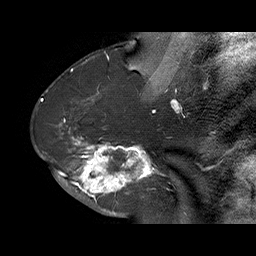
Breast MRI (dynamic contrast-enhanced), one sagittal slice; slice 35 of 70 in the series (ordered by position); dynamic contrast-enhanced series, time point 2 of 6 at this slice position (early post-contrast); 1.5 T; TE 4.5 ms, TR 32.4 ms; 3 mm slice thickness; 256 × 256 image matrix, field of view 180 × 180 mm. Female patient. From the clinical record (not read from this slice): setting: breast cancer imaged before/during neoadjuvant chemotherapy; receptor status: HR-positive, HER2-negative.
Annotated regions visible in this slice (semi-automatically segmented with operator editing):
- analysis volume of interest (the breast-tissue region the enhancement analysis was run in; not a lesion): bounding box <71,128,159,202> (left, top, right, bottom; pixels)
- tumour enhancement mask (voxels above the 100 % enhancement threshold inside the analysis volume of interest): <71,136,159,200>